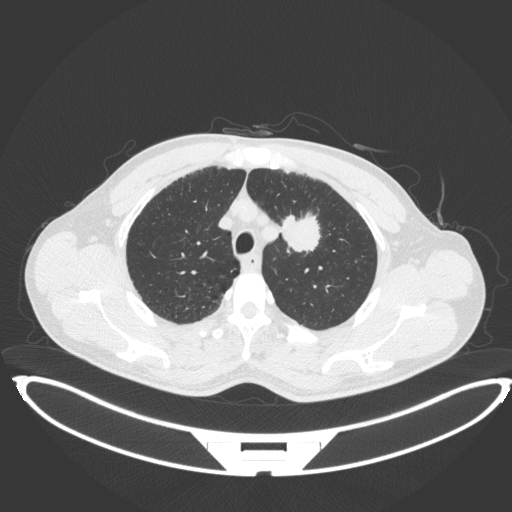
Chest CT, one axial slice. Position 347 of 407 along the scan axis. Reconstruction kernel B31f. Lung window (W 1500 / L -600 HU). 1 mm slice thickness. 512 × 512 image matrix. Patient: male, 60 years. From the clinical record (not read from this slice): clinical TNM (as recorded): T2a N0 M0; histopathological grade: G1-G2.
Annotated regions visible in this slice (rectangle marked by the reading radiologist):
- lung tumour (recorded histology: squamous cell carcinoma): bounding box <280,208,323,258> (left, top, right, bottom; pixels)